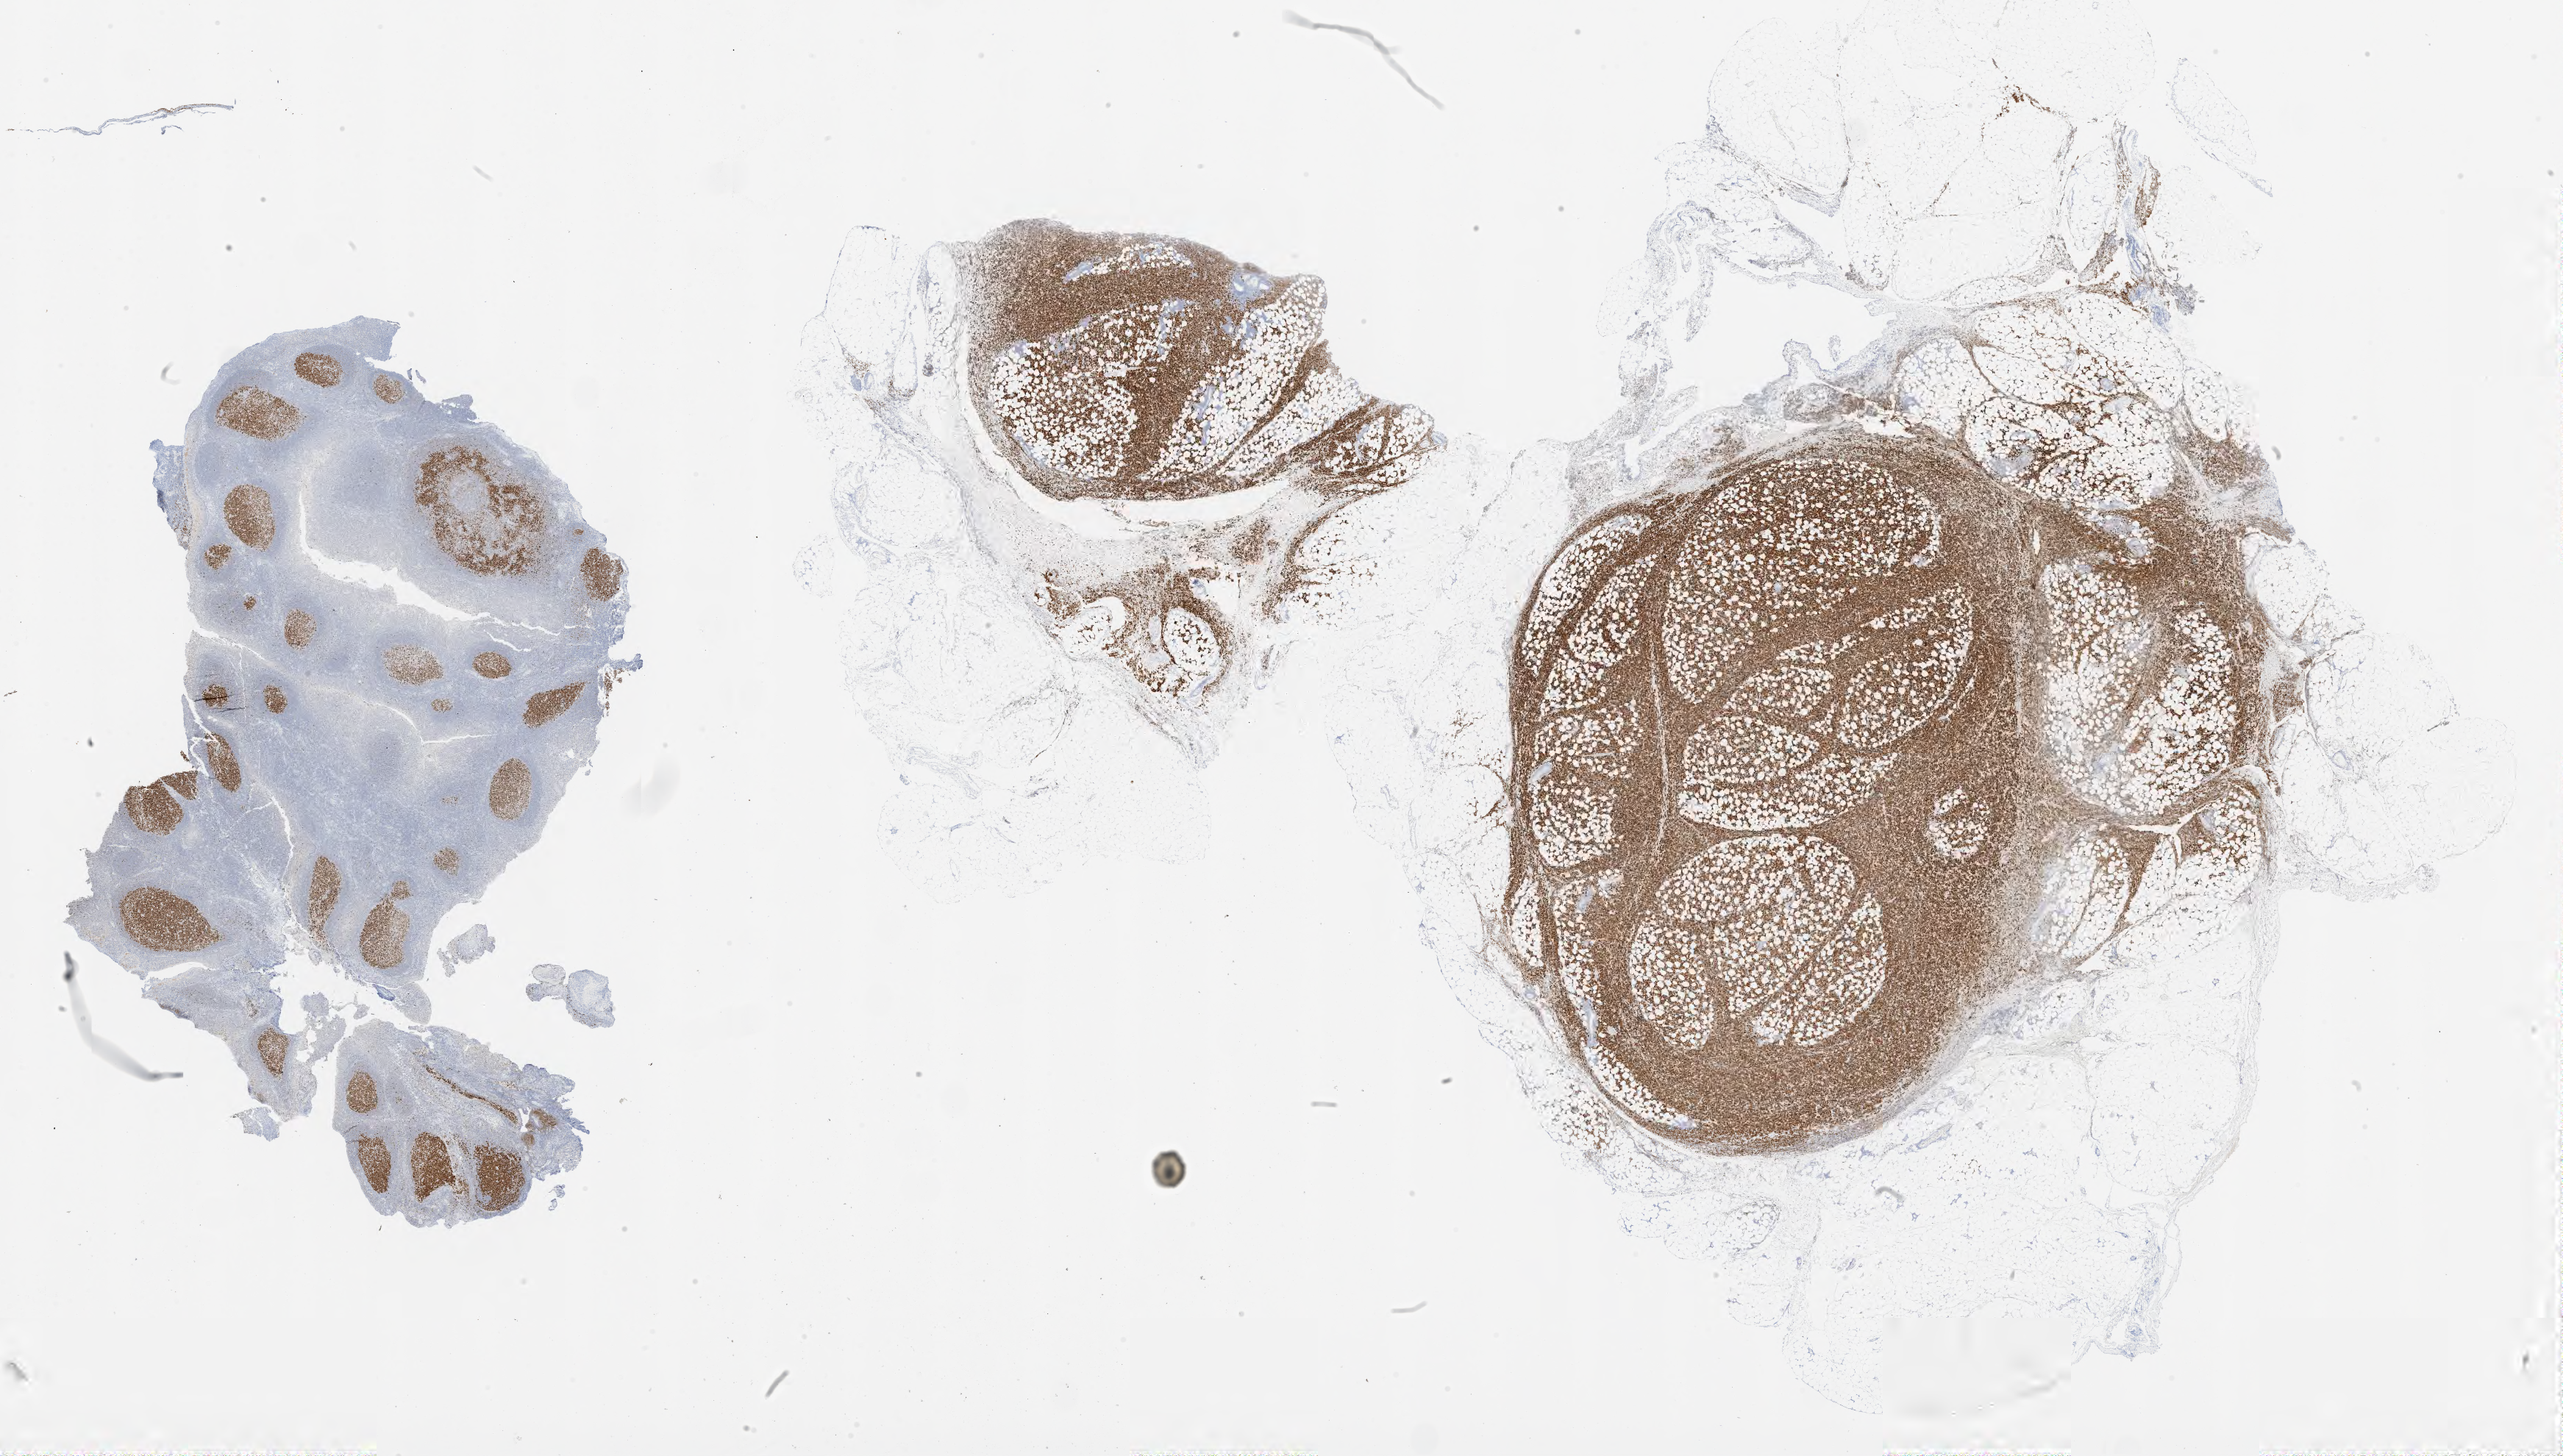
IHC for BCL6, whole-slide image, a low-resolution overview of the entire scanned area, about 28.0 x 15.9 mm. Specimen: tumor tissue. Patient: male, 24 years old.
Diagnosis: Burkitt lymphoma, NOS.